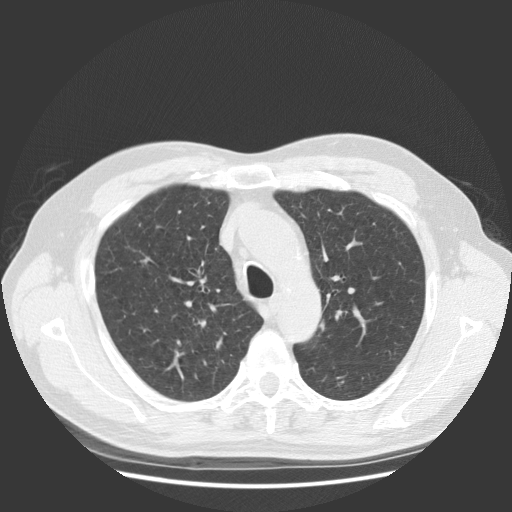
Low-dose screening chest CT, one axial slice. Position 94 of 131 along the scan axis. 140 kVp. Lung window (W 1500 / L -600 HU). 512 × 512 image matrix.
Outlined on this slice (expert manual segmentation):
- lesion 1 (tumor, upper lobe of right lung): bounding box <198,320,206,327> (left, top, right, bottom; pixels)